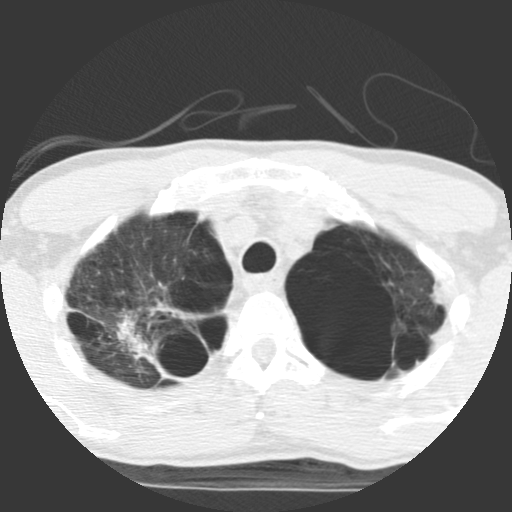
Axial slice from a low-dose chest CT screening exam. First (baseline) screen. Lung window (W 1500 / L -600 HU). 2.5 mm slice thickness. Standard (soft-tissue) reconstruction kernel (STANDARD). Slice 93 of 117 in the series. Male participant, aged 62 years at enrolment.
Expert-annotated lung lesion, bounding box [x1, y1, x2, y2] px = [114, 311, 214, 389]. Screening reader's record for this exam: no non-calcified nodule ≥4 mm recorded. Official screen result: negative screen, minor abnormalities not suspicious for lung cancer. Lung cancer was diagnosed 357 days after this screen (after the second annual screen): non-small cell carcinoma, right upper lobe, poorly differentiated (G3), stage IA (AJCC 6th edition), 70 mm at pathology.